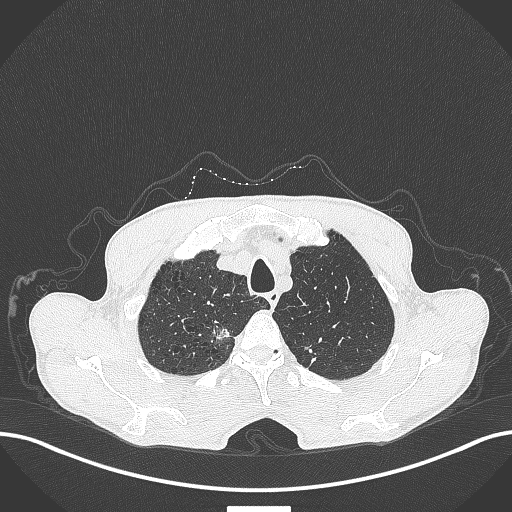
Chest CT, one axial slice; slice 368 of 445 in the series (ordered by position); 120 kVp; lung window (W 1500 / L -600 HU); 1 mm slice thickness; 512 × 512 image matrix. Patient: male, 70 years. From the clinical record (not read from this slice): clinical TNM (as recorded): T1a N0 M0; histopathological grade: G1-2.
Outlined on this slice (bounding box drawn by a radiologist):
- lung tumour (recorded histology: adenocarcinoma): box from (x=210, y=316) to (x=238, y=343) px